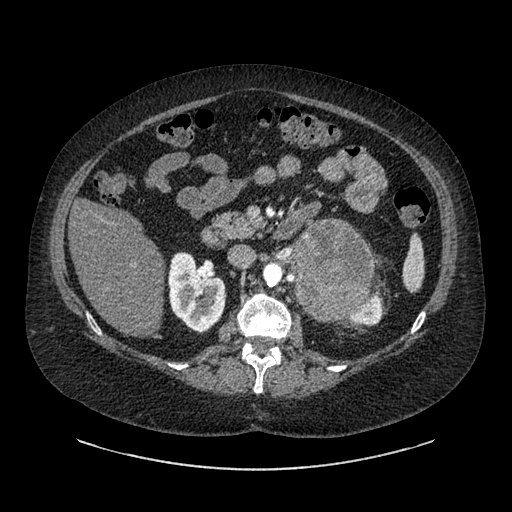
Contrast-enhanced abdominal CT, one axial slice; slice 529 of 769 in the series (ordered by position); intravenous contrast given; soft-tissue window (W 400 / L 40 HU); 0.62 mm slice thickness; 512 × 512 image matrix. Patient: female, 61 years. From the clinical record (not read from this slice): diagnosis: adrenocortical carcinoma; tumour side: left adrenal; tumour size at pathology: 13 cm; Ki-67 index: 79 %; stage (as recorded): 2.
Annotated regions visible in this slice (semi-automatically segmented with operator editing):
- mass: bounding box [x1, y1, x2, y2] px = [297, 222, 375, 317]